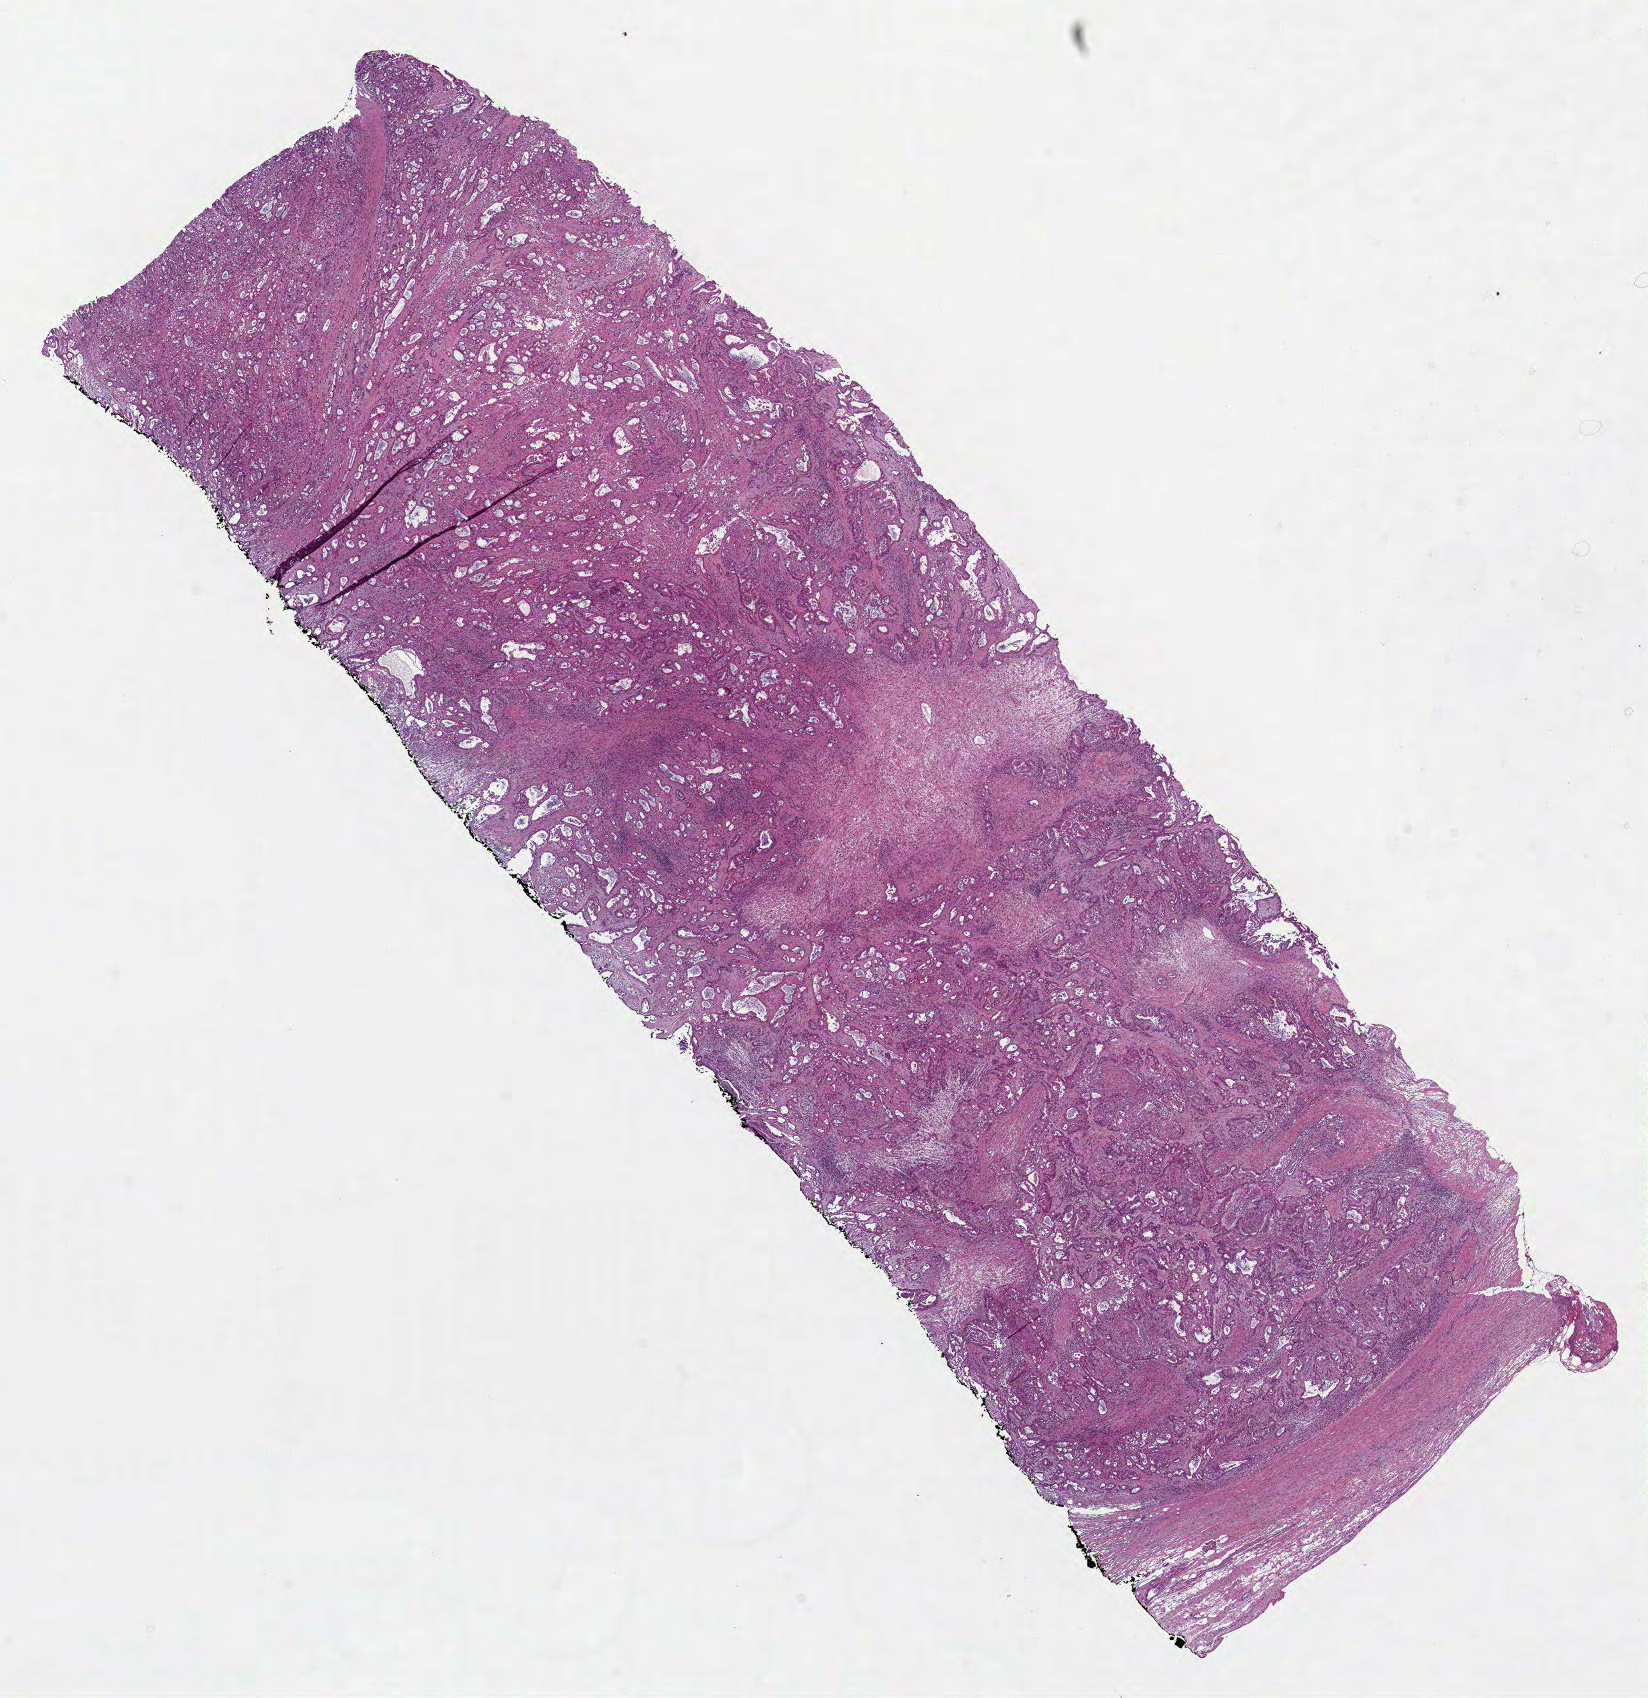
H&E whole-slide image — whole scanned area (about 13.3 x 13.7 mm, slide scanned at 40x) shown as a low-resolution overview, formalin-fixed paraffin-embedded (FFPE) diagnostic section, sample: primary tumour, mesothelium. Male patient; age at initial diagnosis 66 years.
* laterality: right
* histologic diagnosis: Mesothelioma, malignant (pleura, NOS)
* AJCC pathologic stage: II